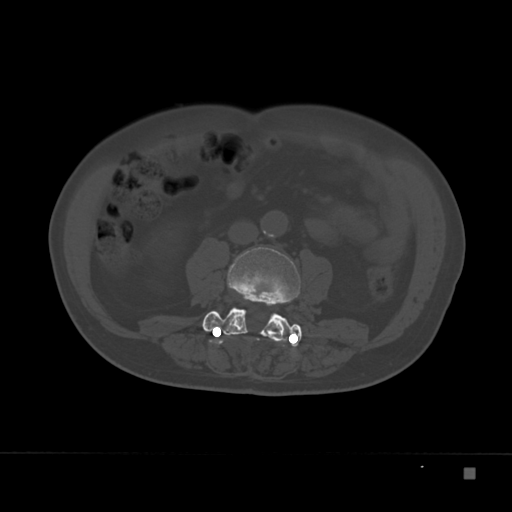
CT including the spine, one axial slice; position 58 of 332 along the scan axis; reconstruction kernel Br40s; 120 kVp; bone window (W 1800 / L 400 HU); 1.5 mm slice thickness; 512 × 512 image matrix, field of view 389 × 389 mm. Male patient, age 72 years. From the clinical record (not read from this slice): primary cancer: skeletal.
Structures marked on this image (semi-automatic segmentation, software-assisted and operator-edited):
- L3 vertebra: box from (x=204, y=247) to (x=302, y=337) px
- L4 vertebra: (x=202, y=297)–(x=302, y=347)